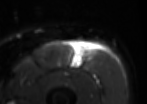
MRI of an extremity soft-tissue mass, one axial slice; slice 35 of 85 in the series (ordered by position); T2-weighted fat-saturated; MR volume resampled by the dataset authors to the PET/CT grid (not the native acquisition matrix); 3.27 mm slice thickness; 147 × 104 image matrix, field of view 144 × 102 mm. Male patient. From the clinical record (not read from this slice): histological type: extraskeletal osteosarcoma; grade: high; site of the primary tumour: thigh.
Outlined on this slice (expert contour drawn on MRI and transferred to this co-registered scan by the dataset authors):
- gross tumour volume (mass): bounding box (x1, y1, x2, y2) in pixels: (72, 44, 86, 68)